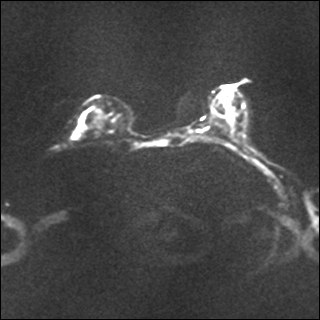
Breast MRI, one axial slice; position 18 of 35 along the scan axis; diffusion-weighted series; image 2 of 4 stored at this slice position (different b-values; order by instance number); 1.5 T; 4 mm slice thickness; 320 × 320 image matrix, field of view 317 × 317 mm. Female patient.
Outlined on this slice (outlined manually by an expert reader):
- tumour on diffusion-weighted imaging: bounding box <74,113,87,139> (left, top, right, bottom; pixels)